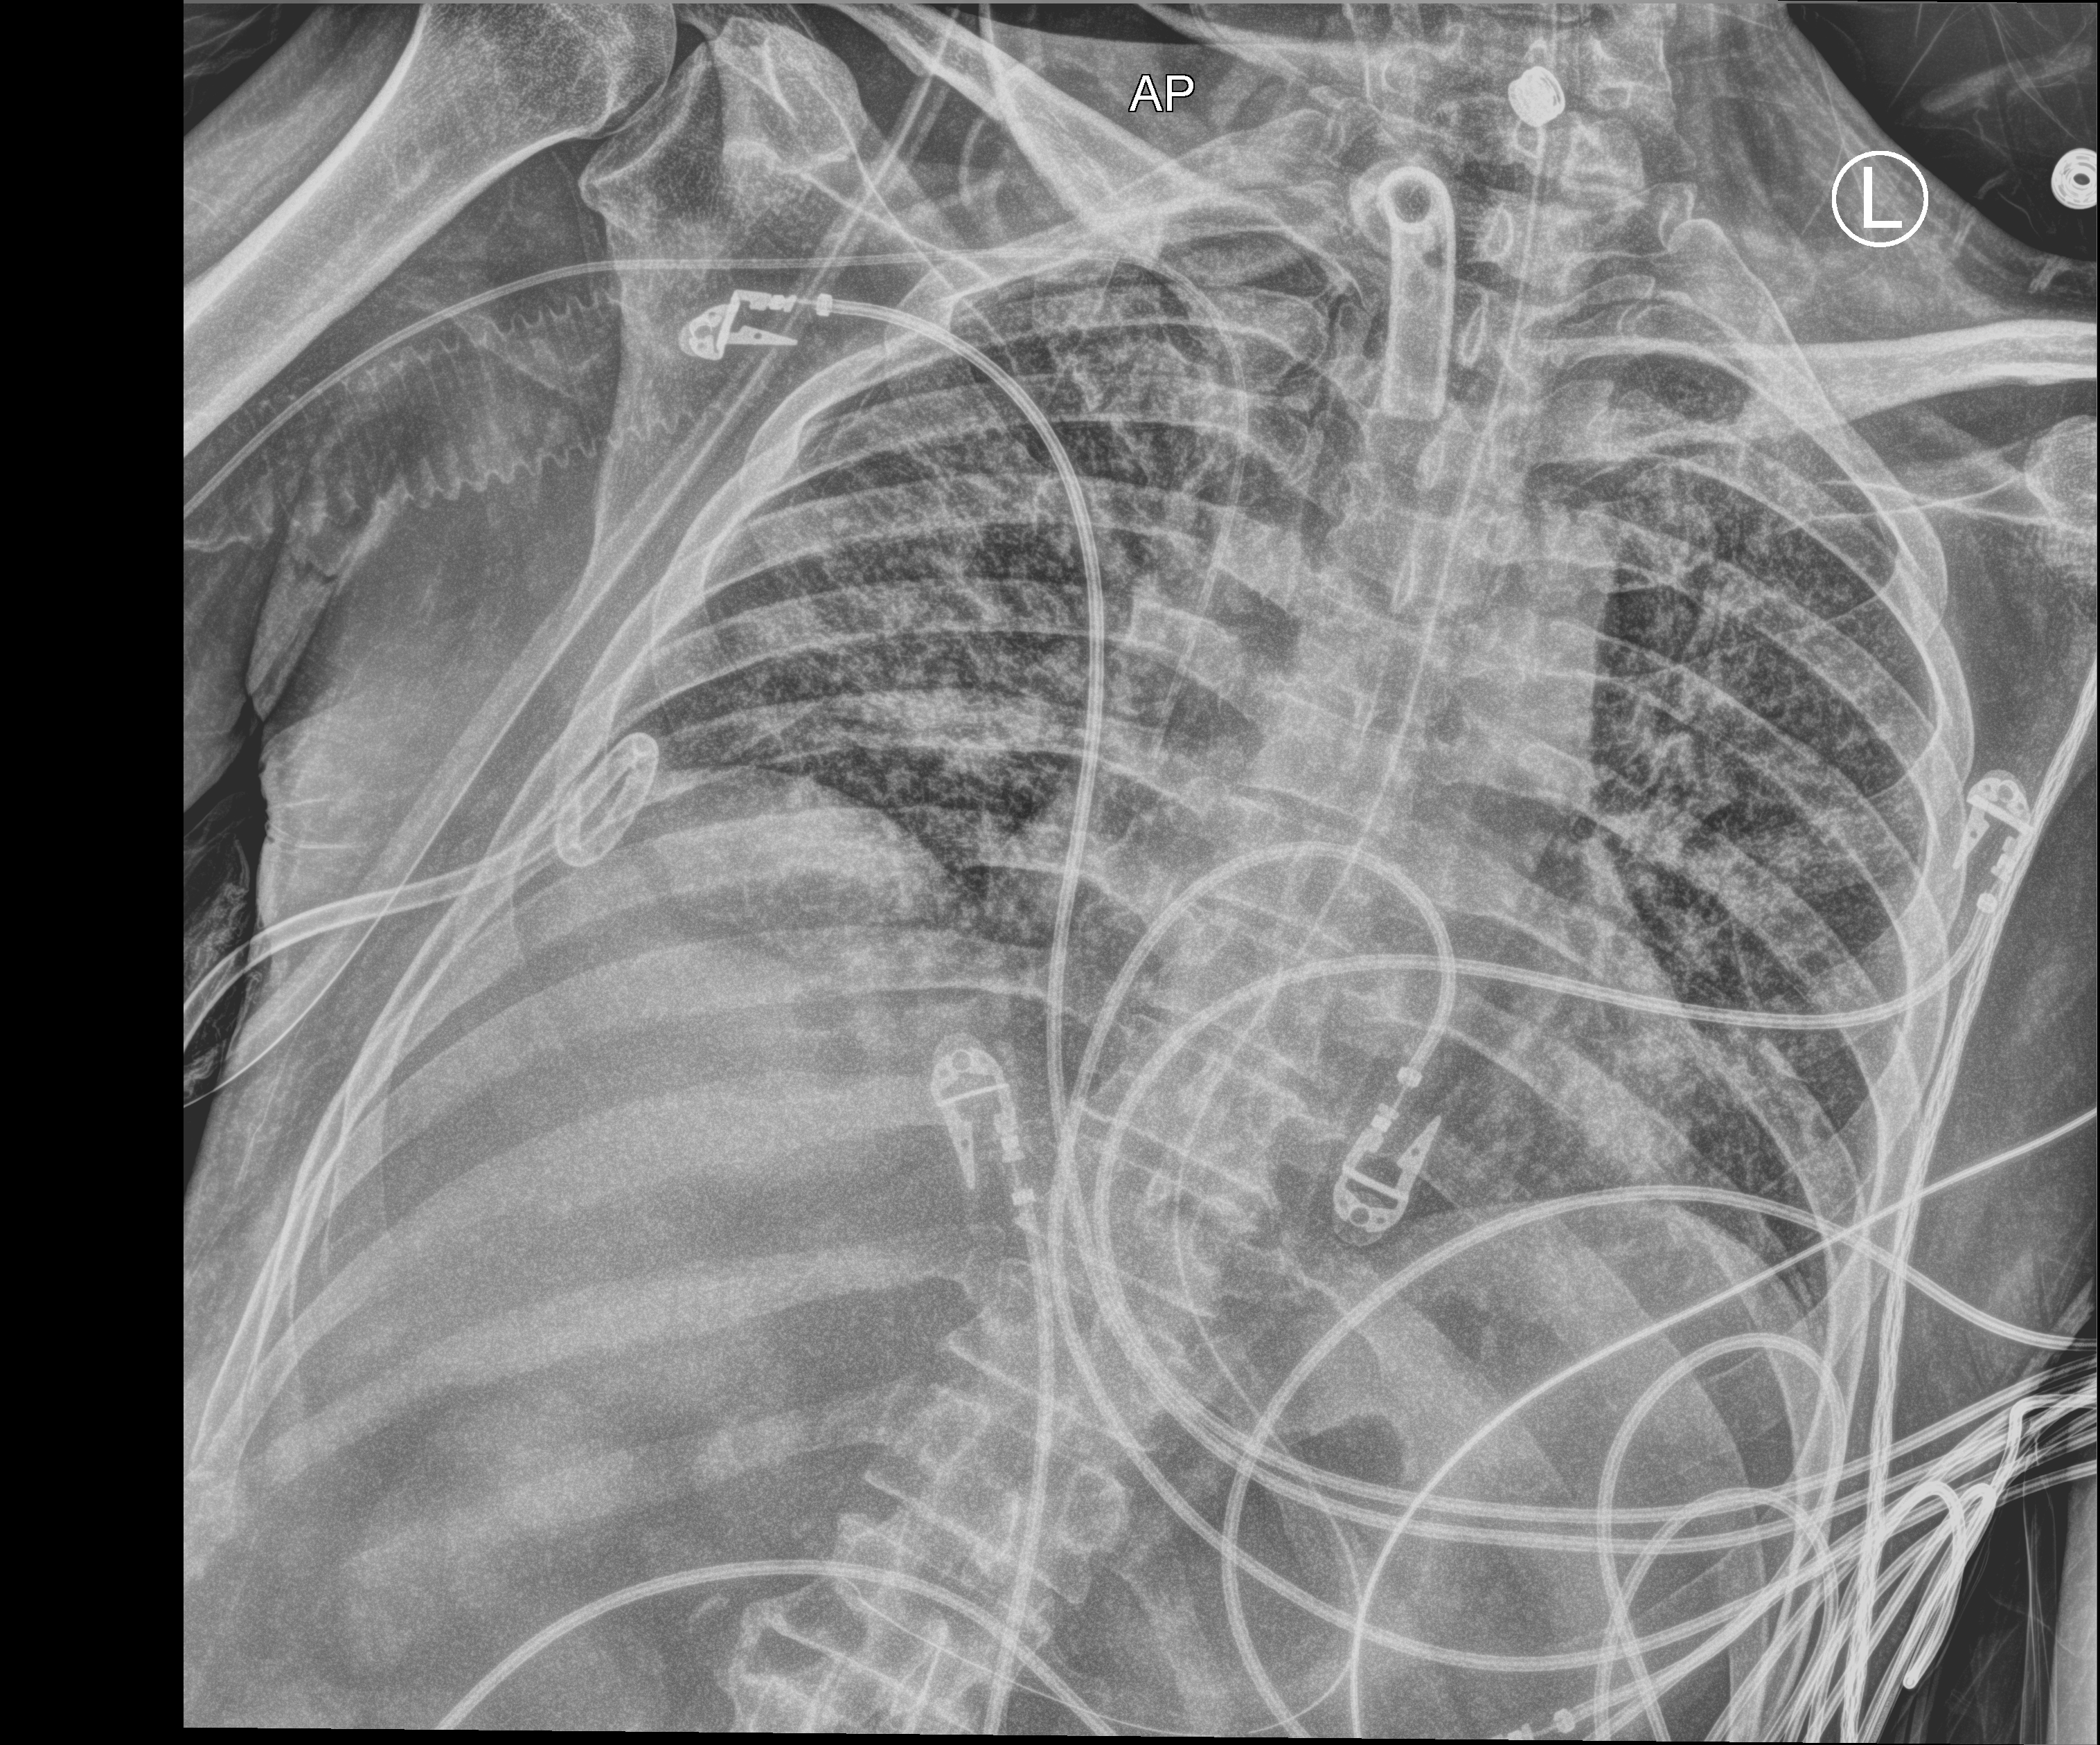
Bedside chest radiograph (computed radiography). Patient hospitalised with COVID-19; male, aged 18–59 years.
Admission-level facts for this patient (not findings on this image; timing relative to this image not recorded): other chronic lung disease (admission record): no.